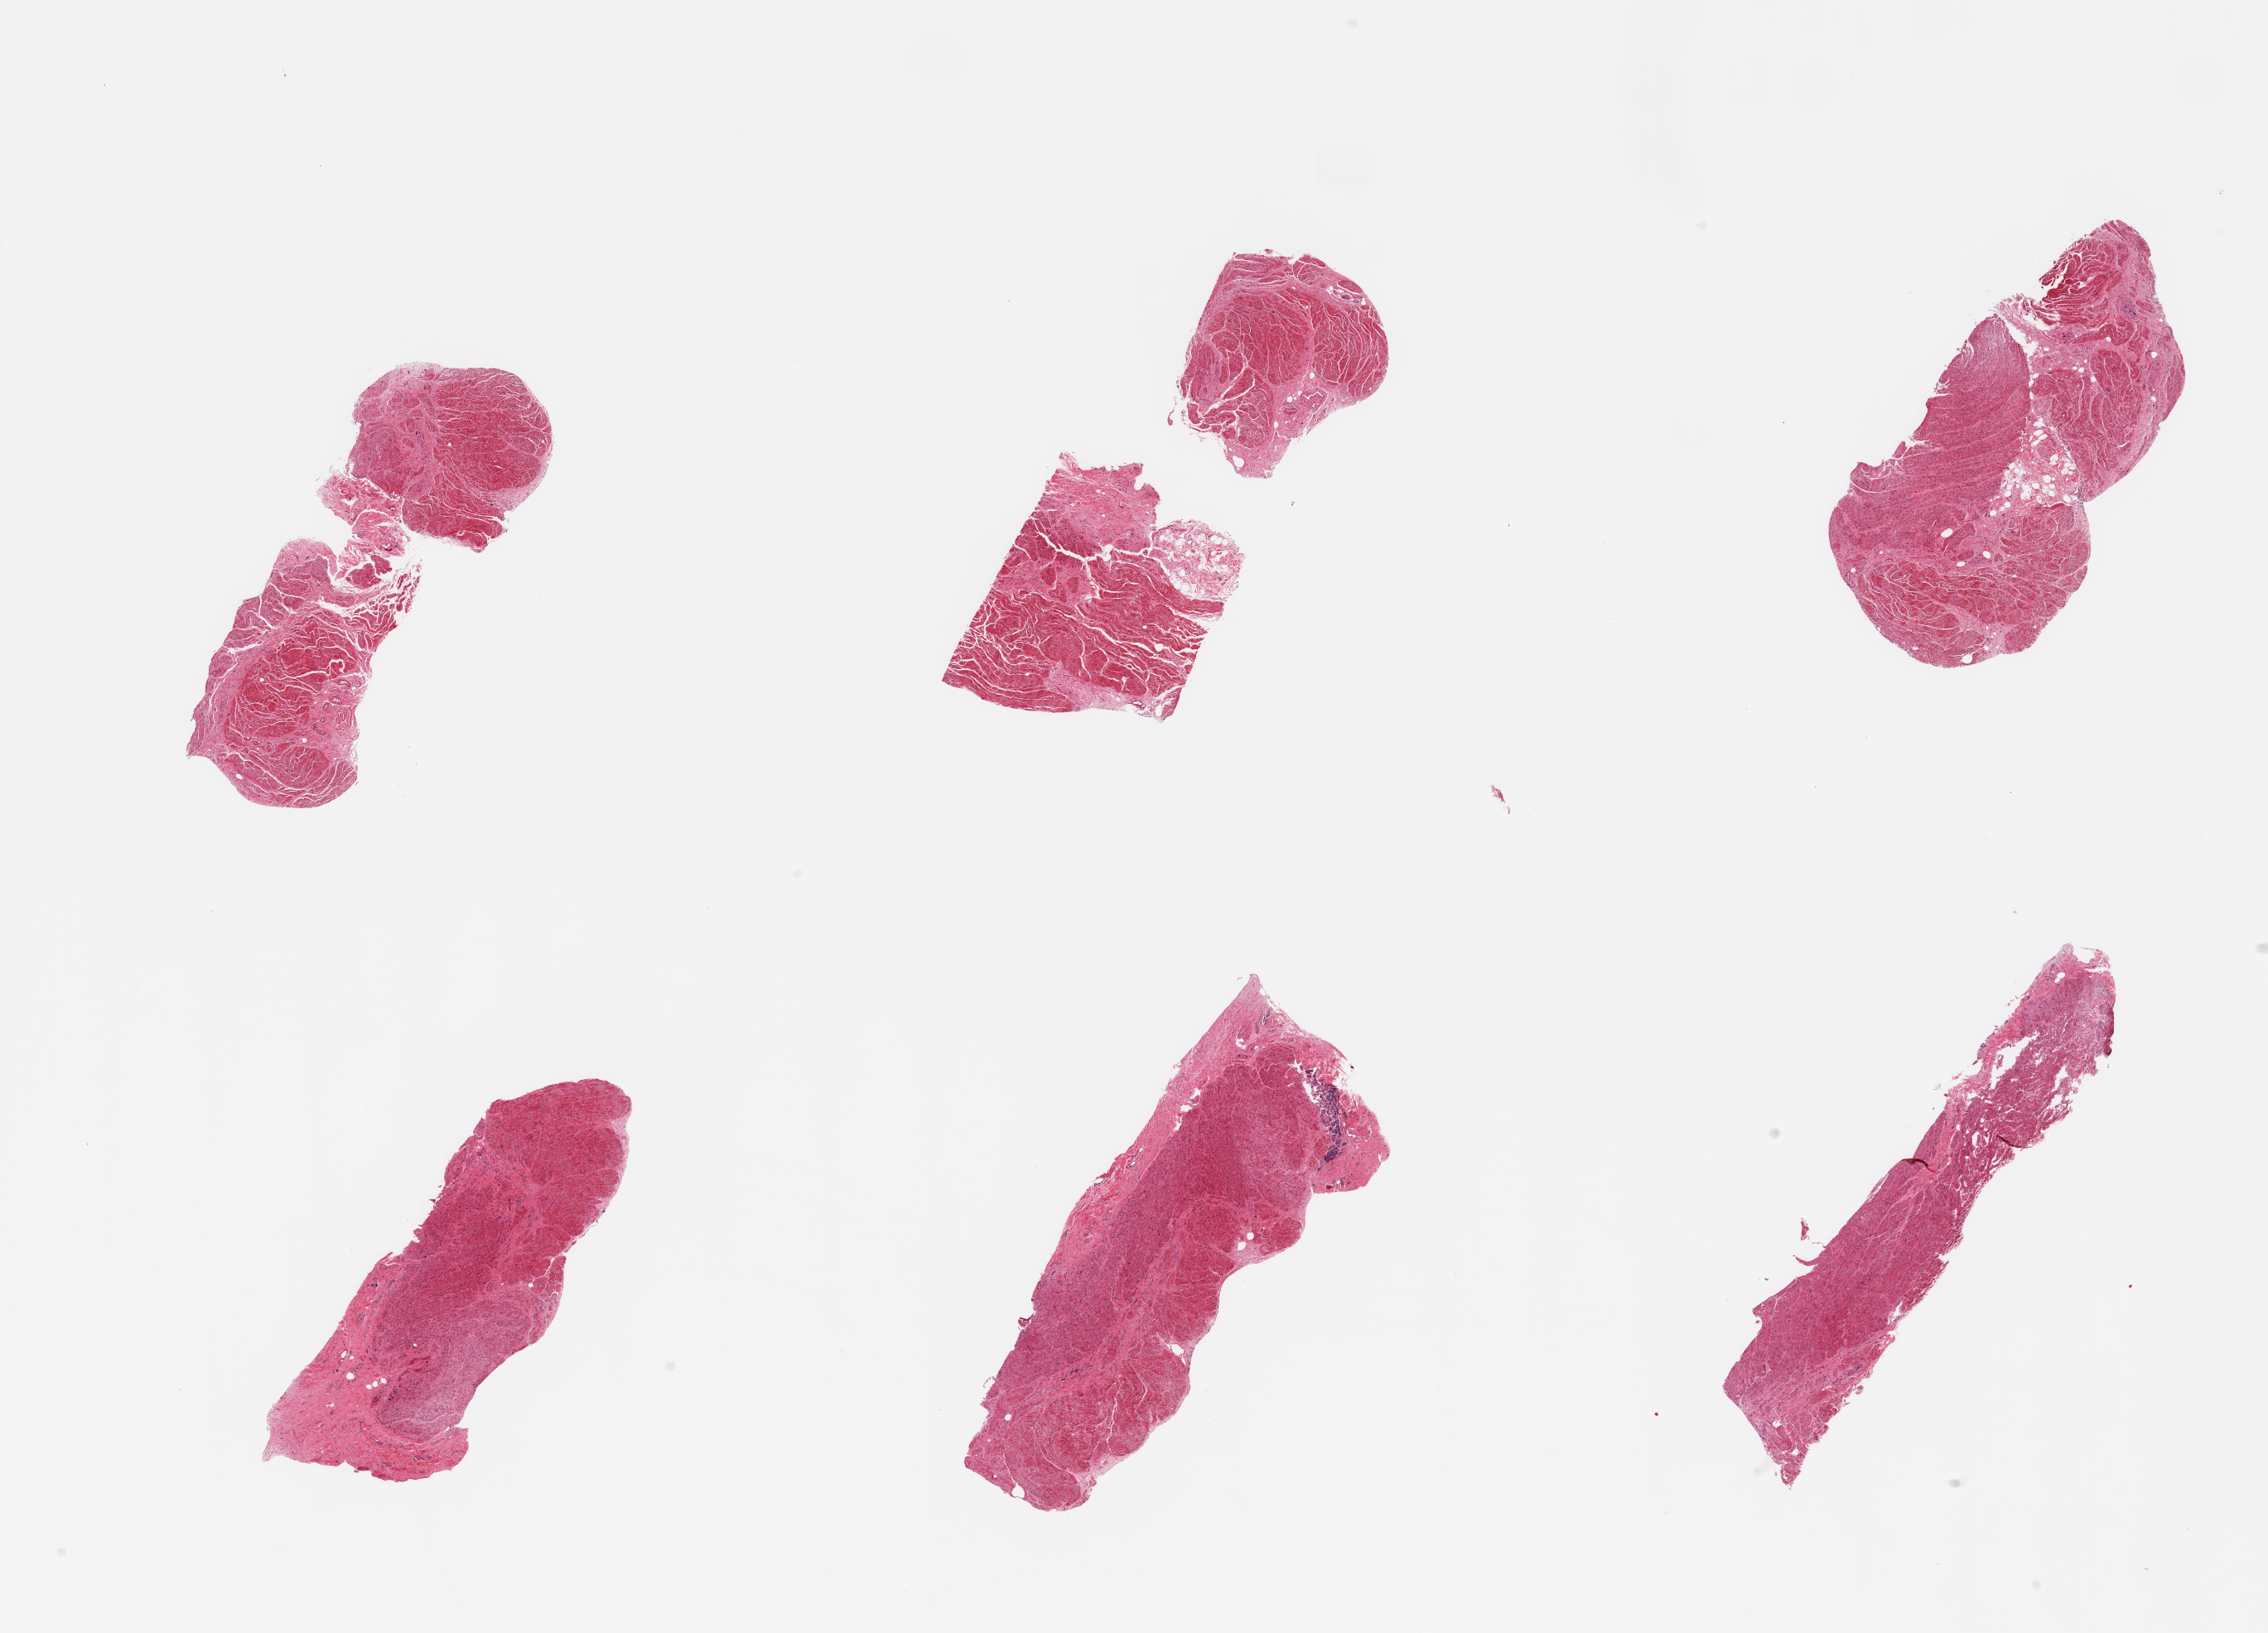
Digitized hematoxylin and eosin (H&E)-stained section — whole scanned area (about 21.7 x 15.6 mm) shown as a low-resolution overview; PAXgene-fixed paraffin-embedded (PFPE) section; target tissue: gastroesophageal junction; donor tissue sample. Donor: male.
Pathologist's review note for this sample: 6 pieces, confirmed target muscularis.